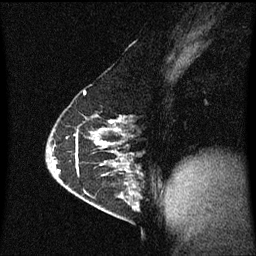
Breast MRI (dynamic contrast-enhanced), one sagittal slice. Slice 35 of 60 in the series (ordered by position). Dynamic contrast-enhanced series, image 2 of 3 at this slice position (ordered by acquisition). 1.5 T. TE 4.2 ms, TR 8.4 ms. 2 mm slice thickness. 256 × 256 image matrix. Female patient, age 63 years.
Outlined on this slice (semi-automatic segmentation, software-assisted and operator-edited):
- analysis volume of interest (the breast-tissue region the enhancement analysis was run in; not a lesion): bounding box (x1, y1, x2, y2) in pixels: (98, 168, 143, 217)
- tumour enhancement mask (voxels above the 70 % enhancement threshold inside the analysis volume of interest): (120, 170, 141, 211)